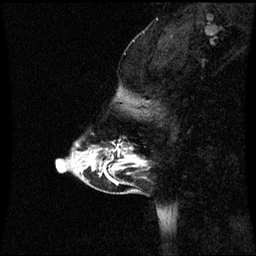
Breast MRI (dynamic contrast-enhanced), one sagittal slice. Position 14 of 60 along the scan axis. Dynamic contrast-enhanced series, image 2 of 3 at this slice position (ordered by acquisition). 1.5 T. TE 4.2 ms, TR 8.9 ms. 2 mm slice thickness. 256 × 256 image matrix, field of view 220 × 220 mm. Female patient, age 43 years. Case-level facts recorded for this patient, not image findings: setting: breast cancer imaged before/during neoadjuvant chemotherapy; receptor status: HR-positive, HER2-negative.
Structures marked on this image (semi-automatically segmented with operator editing):
- analysis volume of interest (the breast-tissue region the enhancement analysis was run in; not a lesion): bounding box <84,144,144,171> (left, top, right, bottom; pixels)
- tumour enhancement mask (voxels above the 70 % enhancement threshold inside the analysis volume of interest): <104,148,107,171>